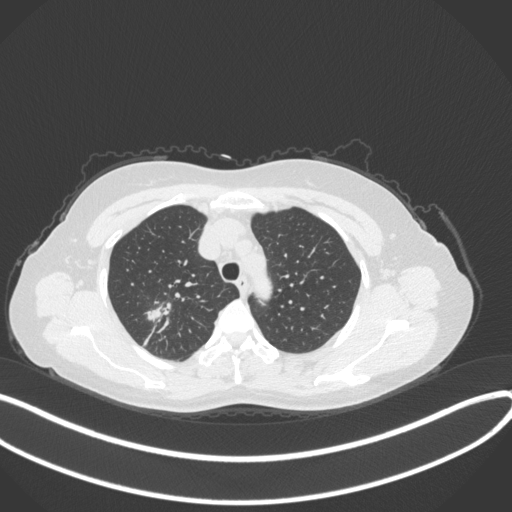
Chest CT, one axial slice; slice 285 of 342 in the series (ordered by position); lung window (W 1500 / L -600 HU); 1 mm slice thickness; 512 × 512 image matrix. Female patient, age 50 years. From the clinical record (not read from this slice): clinical TNM (as recorded): T1c N0 M0; histopathological grade: G2-3.
Structures marked on this image (bounding box drawn by a radiologist):
- lung tumour (recorded histology: adenocarcinoma): bounding box <143,301,169,324> (left, top, right, bottom; pixels)